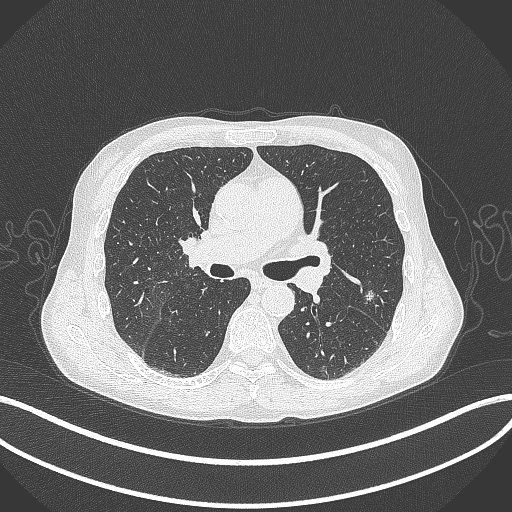
Chest CT, one axial slice; position 214 of 429 along the scan axis; 120 kVp; lung window (W 1500 / L -600 HU); 1 mm slice thickness; 512 × 512 image matrix, field of view 400 × 400 mm. Patient: male, 58 years. Case-level facts recorded for this patient, not image findings: clinical TNM (as recorded): T1c N0 M0; histopathological grade: G2.
Annotated regions visible in this slice (rectangle marked by the reading radiologist):
- lung tumour (recorded histology: adenocarcinoma): bounding box <362,286,379,305> (left, top, right, bottom; pixels)